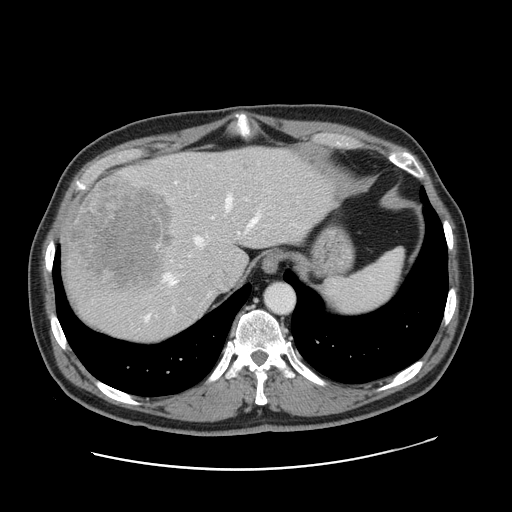
Contrast-enhanced abdominal CT, one axial slice. Slice 129 of 178 in the series (ordered by position). 120 kVp. Intravenous contrast given. Soft-tissue window (W 400 / L 40 HU). 2.5 mm slice thickness. 512 × 512 image matrix. Male patient, age 63 years. Case-level facts recorded for this patient, not image findings: diagnosis: colorectal cancer liver metastases, imaged before liver resection; multiple liver metastases: yes; largest metastasis: 8 cm; disease in both lobes: yes.
Annotated regions visible in this slice (expert manual segmentation):
- hepatic veins: bounding box (x1, y1, x2, y2) in pixels: (146, 196, 258, 320)
- liver: (62, 148, 332, 342)
- planned liver remnant (the part of the liver to remain after resection): (153, 150, 331, 278)
- portal vein (with intrahepatic branches): (157, 182, 214, 247)
- liver metastasis: (244, 165, 248, 169)
- liver metastasis: (69, 182, 174, 288)